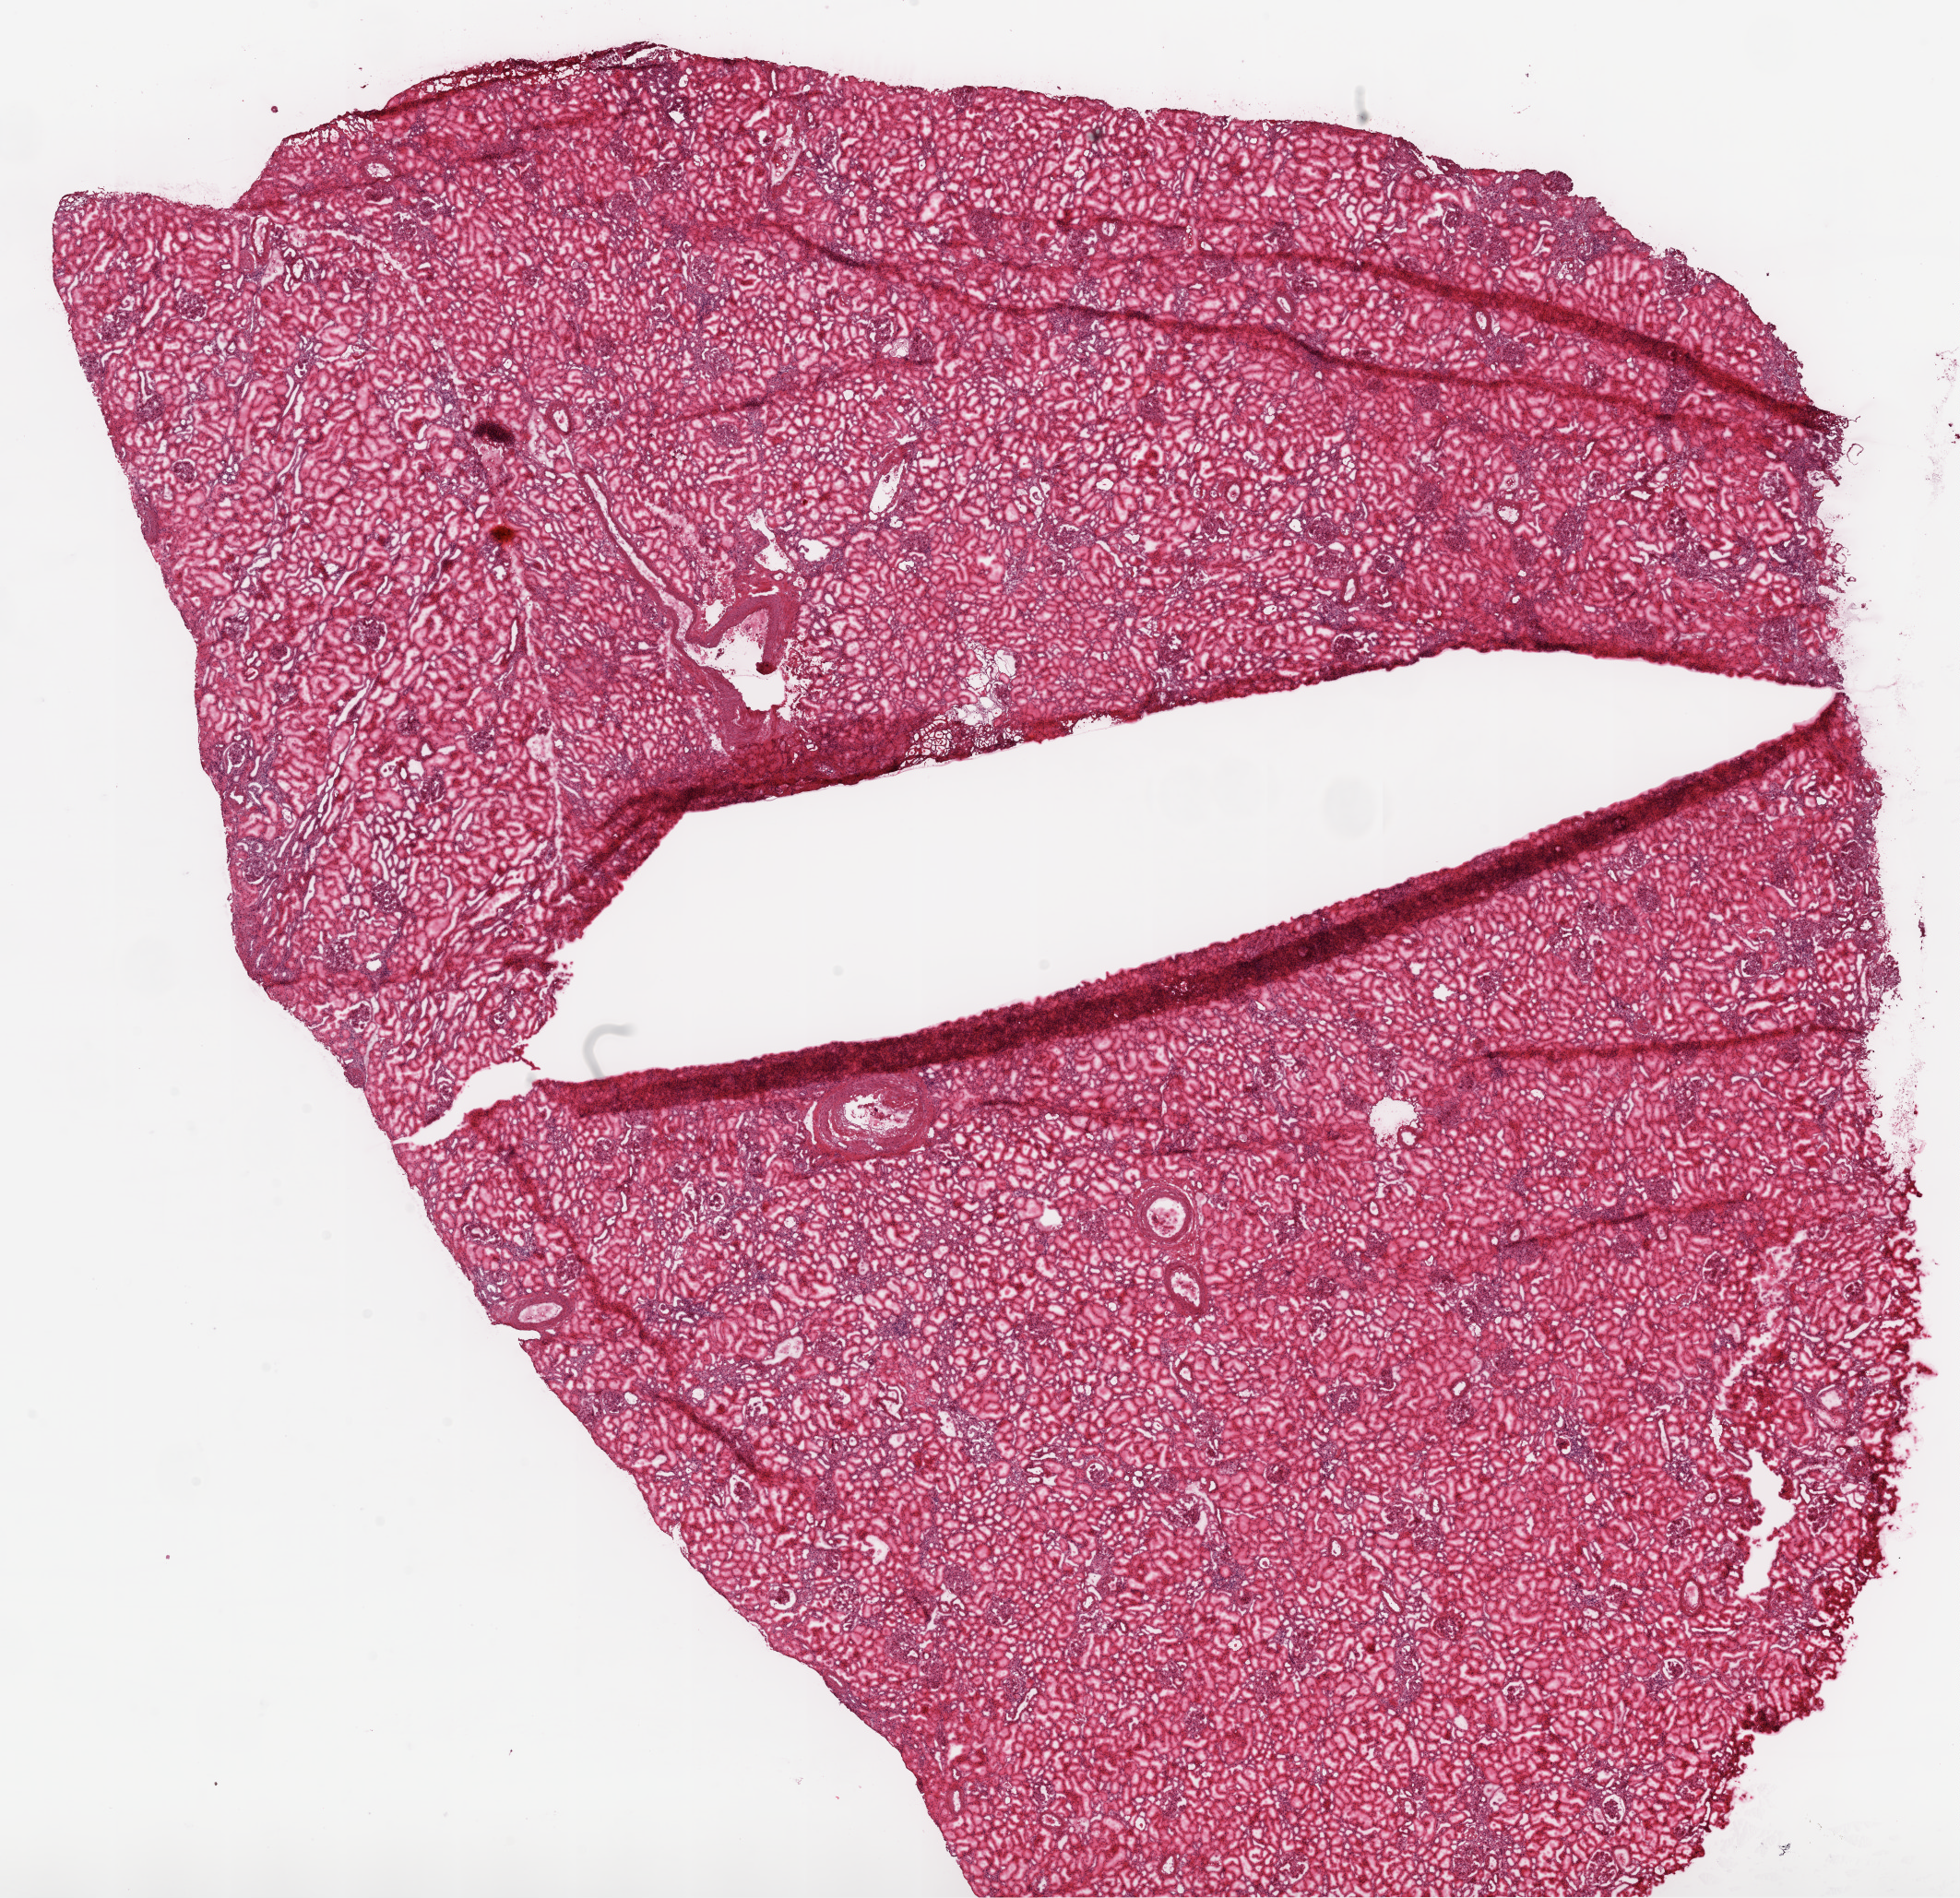
Whole-slide histology image, H&E — low-resolution overview of the scanned area, about 17.1 x 16.5 mm (acquisition: 20x scan), frozen section from the top of the tissue portion, solid tissue normal (non-tumour tissue) sample from the kidney. Patient: male, age at initial diagnosis 67 years.
- this section: solid tissue normal sample (biorepository sample class)
- patient diagnosis: Clear cell adenocarcinoma, NOS